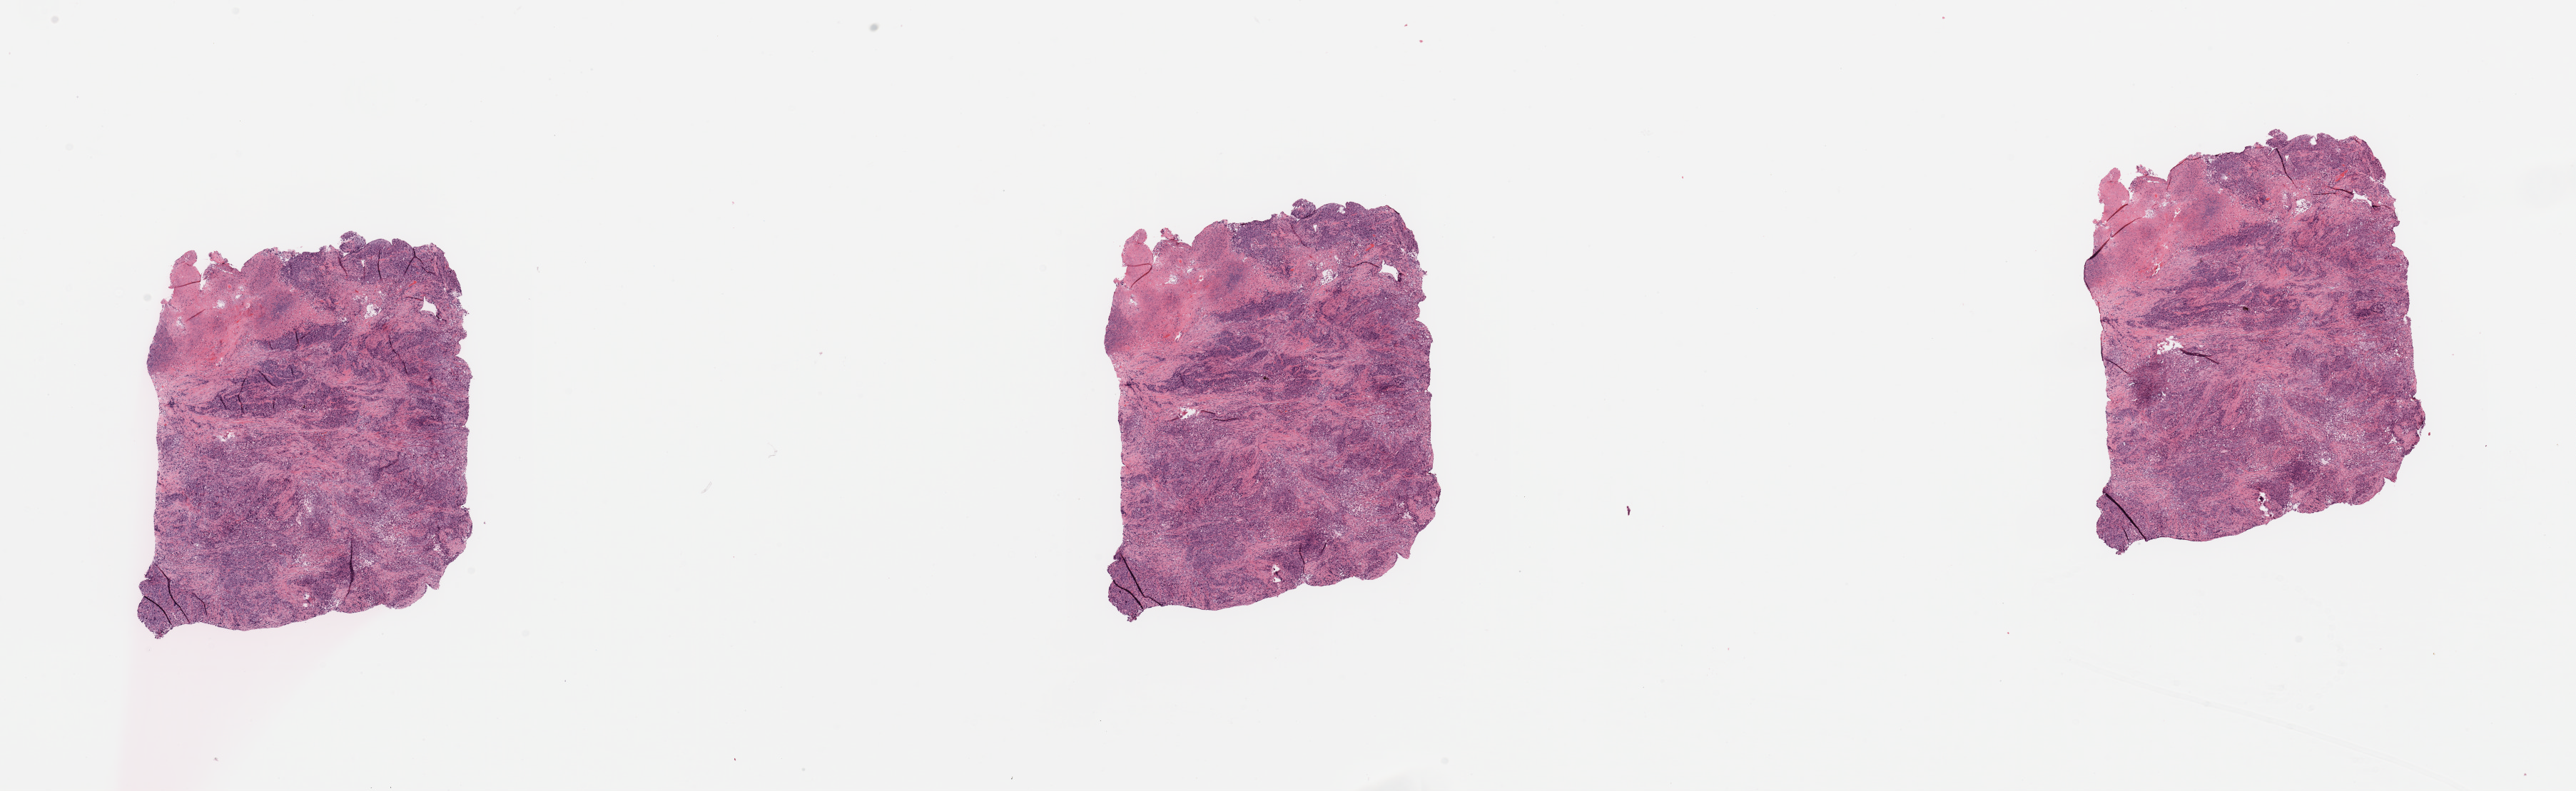
Digitized Hematoxylin and eosin (H&E) stained tissue section (whole slide) — whole scanned area (about 28.5 x 8.8 mm, from a 20x scan) shown as a low-resolution overview; tumour tissue sample, pancreas. Female, 52 y/o. Histologic grade: G3 (poorly differentiated).
Primary tumour site (as recorded): head. AJCC pathologic stage: IIB. Histologic diagnosis: Infiltrating duct carcinoma, NOS.